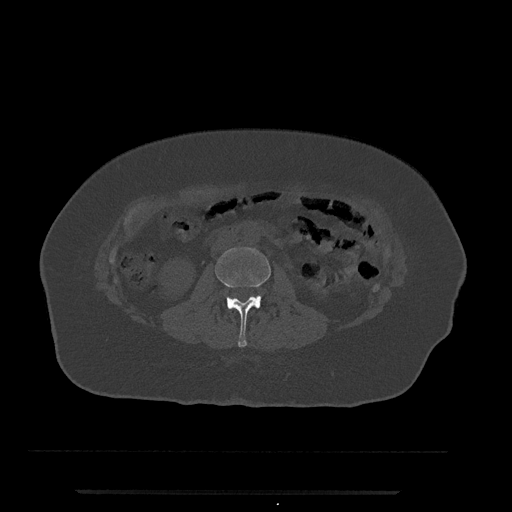
CT including the spine, one axial slice; slice 24 of 797 in the series (ordered by position); reconstruction kernel Br40s/3; bone window (W 1800 / L 400 HU); 0.5 mm slice thickness; 512 × 512 image matrix. Female patient, age 51 years. Case-level facts recorded for this patient, not image findings: primary cancer: neuro; vertebrae with lytic lesions (as recorded): T8.
Structures marked on this image (semi-automatic segmentation, software-assisted and operator-edited):
- L2 vertebra: bounding box (x1, y1, x2, y2) in pixels: (215, 247, 271, 347)